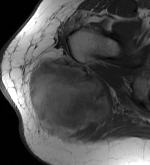
MRI of an extremity soft-tissue mass, one axial slice. Slice 32 of 56 in the series (ordered by position). MR volume resampled by the dataset authors to the PET/CT grid (not the native acquisition matrix). 3.27 mm slice thickness. 150 × 165 image matrix, field of view 146 × 161 mm. Female patient. Case-level facts recorded for this patient, not image findings: histological type: epithelioid sarcoma with vascular differentiation; site of the primary tumour: right buttock.
Annotated regions visible in this slice (expert contour drawn on MRI and transferred to this co-registered scan by the dataset authors):
- gross tumour volume (mass): bounding box <25,54,113,141> (left, top, right, bottom; pixels)